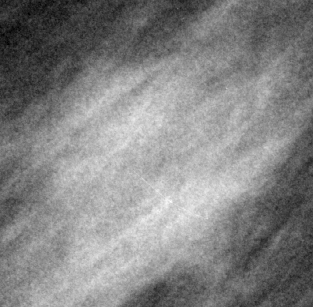
Crop from a digitized film mammogram around one marked abnormality; right breast; MLO view; BI-RADS breast density category 2 (scale 1–4).
Marked abnormality: mass, shape irregular, margins spiculated; BI-RADS assessment category 4; pathology (as recorded): malignant.